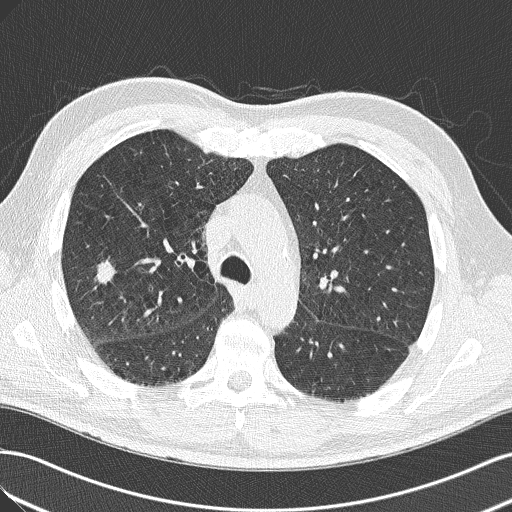
Low-dose screening chest CT, one axial slice. Slice 91 of 143 in the series (ordered by position). Reconstruction kernel B50f. Lung window (W 1500 / L -600 HU). 2 mm slice thickness. 512 × 512 image matrix, field of view 360 × 360 mm.
Annotated regions visible in this slice (expert manual segmentation):
- lesion 1 (tumor, lower lobe of right lung): bounding box <96,261,116,284> (left, top, right, bottom; pixels)